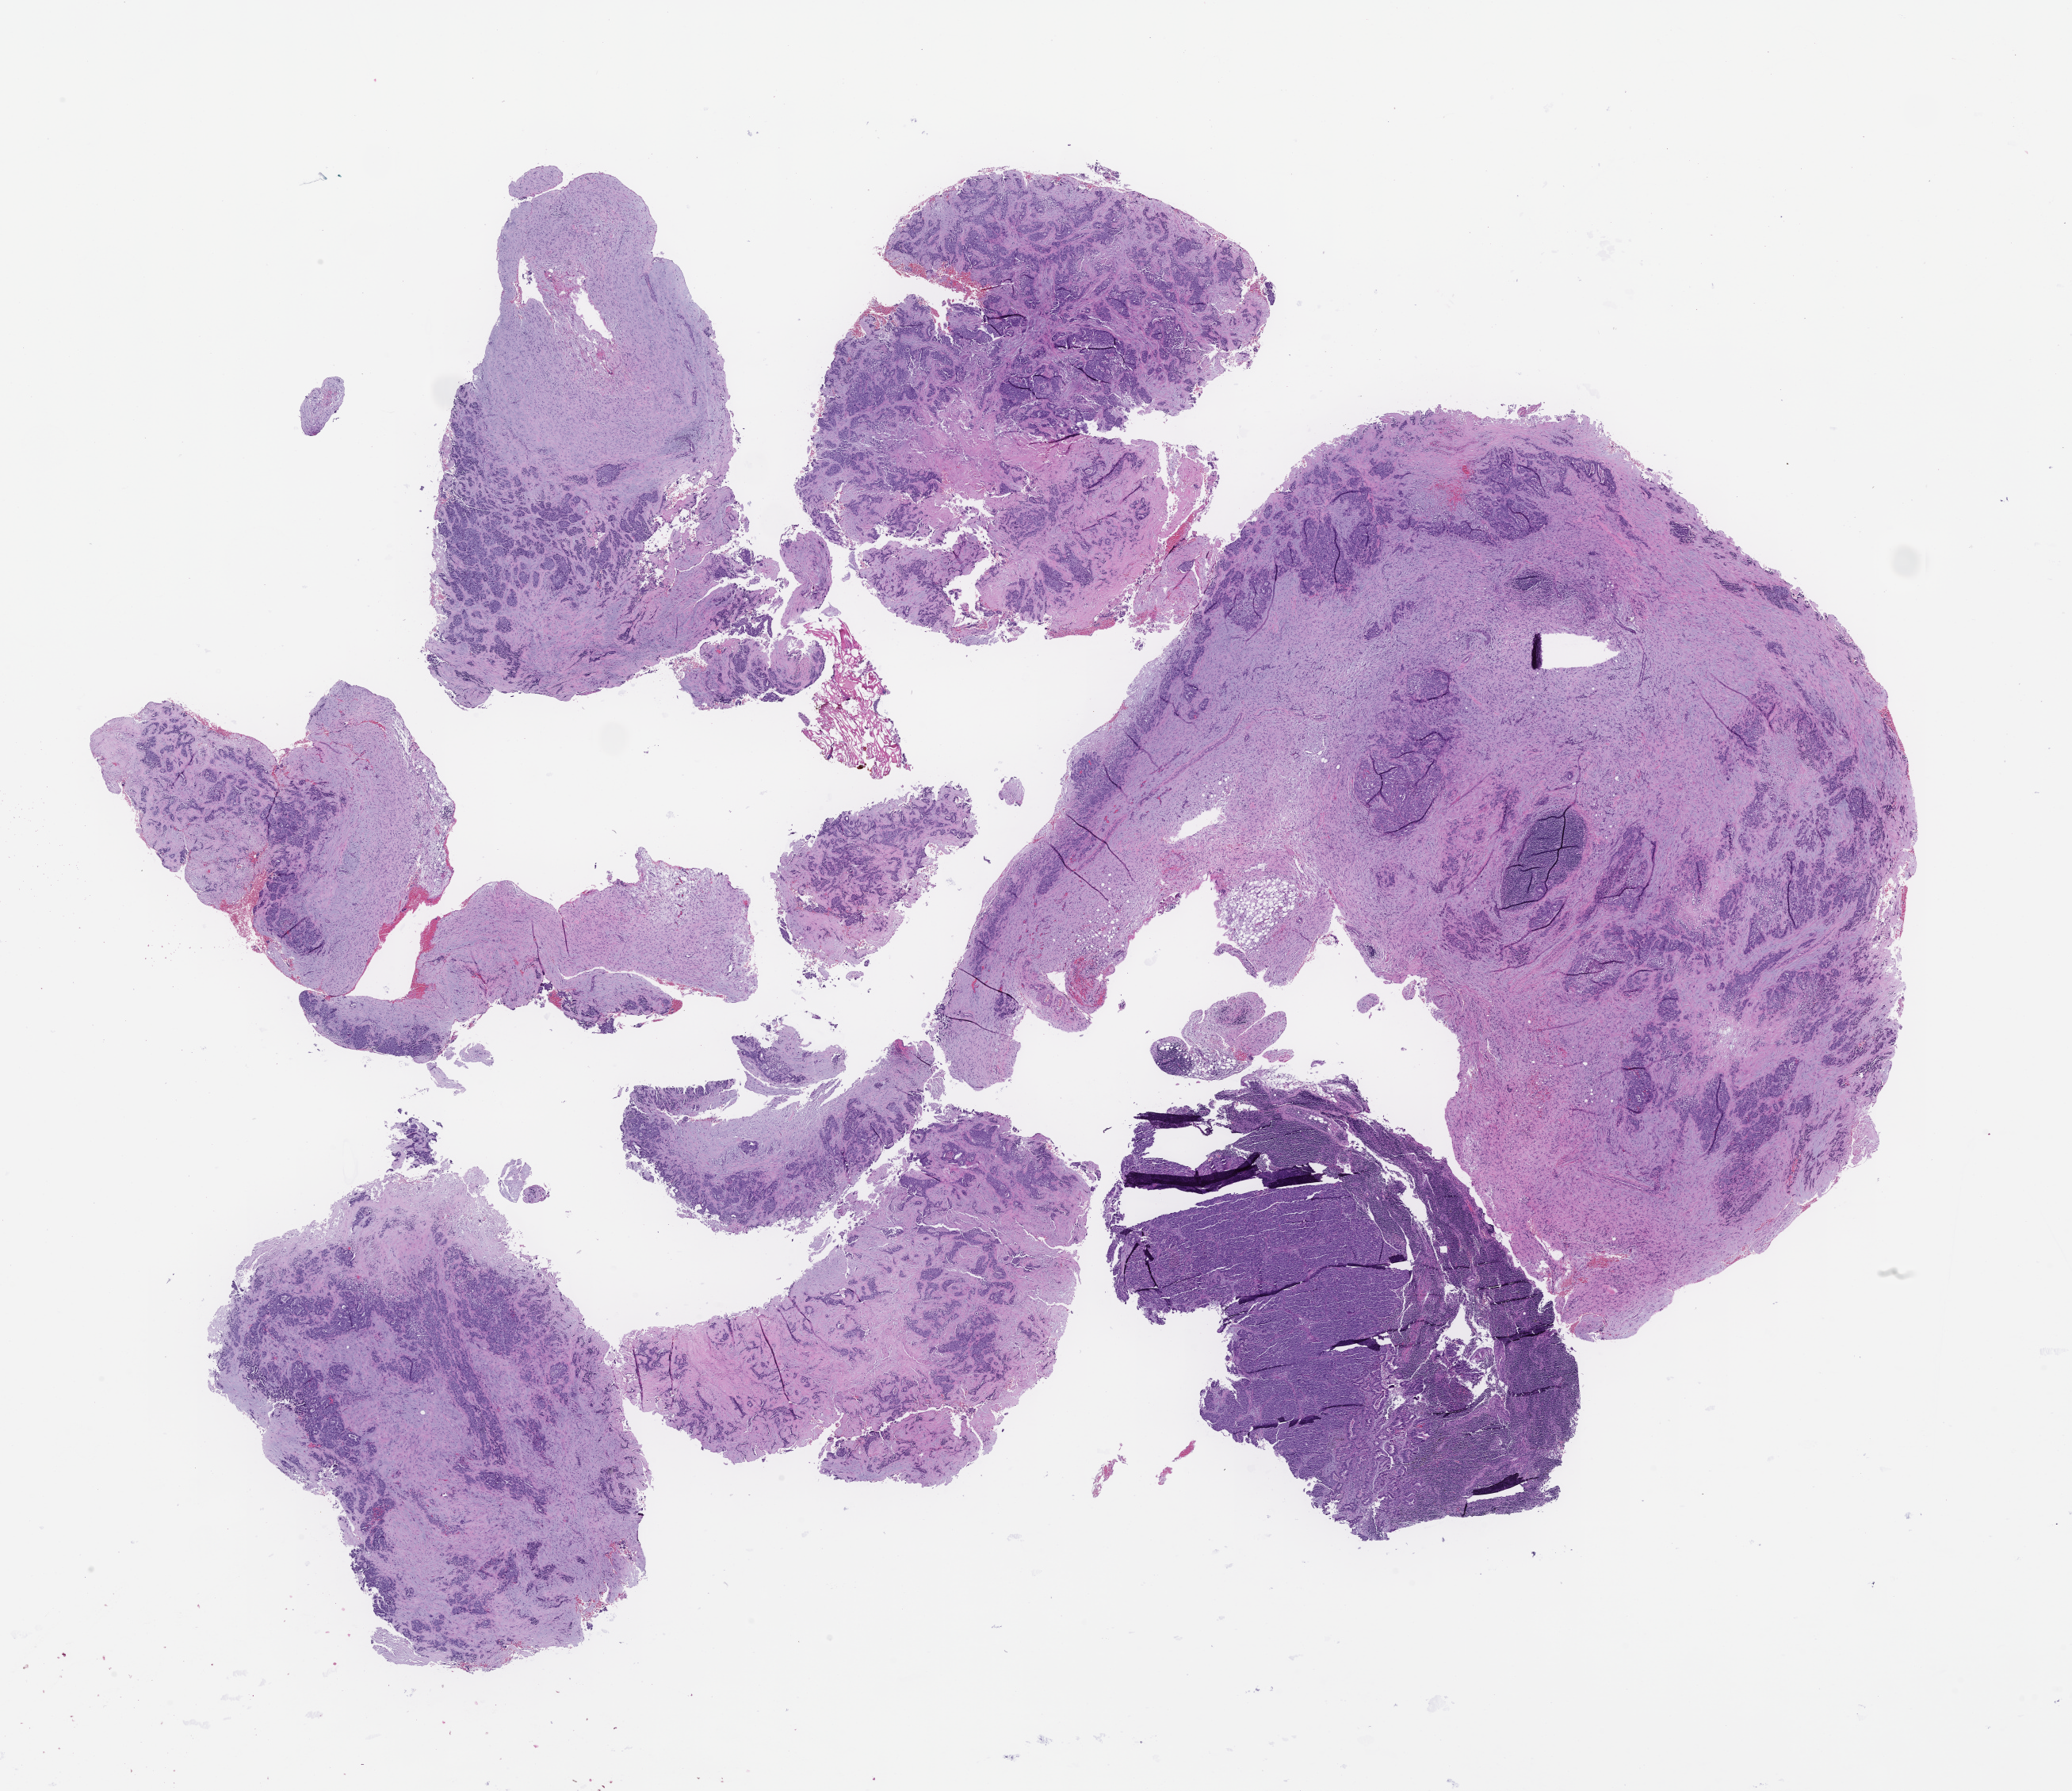
H&E whole-slide image — shown as a low-resolution overview of the whole scanned area (about 21.1 x 18.2 mm). Formalin-fixed paraffin-embedded section. Archival tissue. Male patient.
This section: metastasis (sampled organ not recorded). Primary diagnosis of the patient: Adenocarcinoma of the Gastroesophageal Junction.